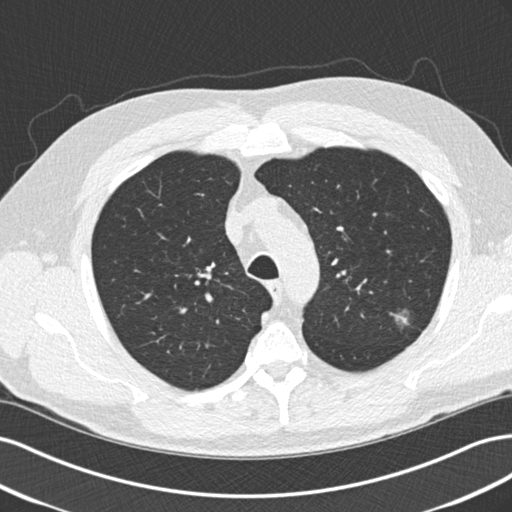
Low-dose screening chest CT, one axial slice. Slice 162 of 209 in the series (ordered by position). Reconstruction kernel B30f. Lung window (W 1500 / L -600 HU). 2 mm slice thickness. 512 × 512 image matrix, field of view 360 × 360 mm.
Outlined on this slice (expert manual segmentation):
- lesion 1 (tumor, upper lobe of left lung): box from (x=393, y=310) to (x=409, y=328) px